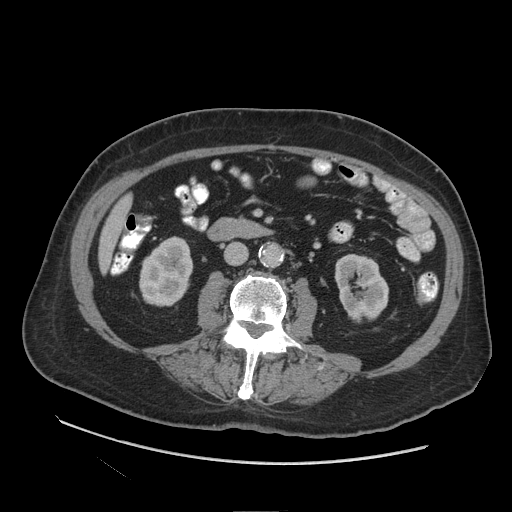
Contrast-enhanced abdominal CT (liver protocol), one axial slice. Slice 23 of 109 in the series (ordered by position). Reconstruction kernel STANDARD. Soft-tissue window (W 400 / L 40 HU). 512 × 512 image matrix, field of view 420 × 420 mm. From the clinical record (not read from this slice): diagnosis: hepatocellular carcinoma (patient treated with transarterial chemoembolisation; whether this scan precedes or follows treatment is not stated here); TNM stage (as recorded): Stage-I; Child-Pugh class: A.
Annotated regions visible in this slice (semi-automatically segmented with operator editing):
- liver parenchyma outside the tumour (the mass and vessels are separate outlines, so this box may not span the whole liver): bounding box <98,194,132,271> (left, top, right, bottom; pixels)